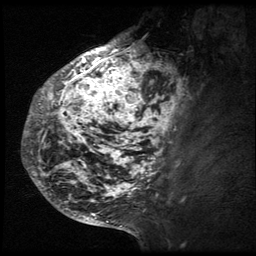
Breast MRI (dynamic contrast-enhanced), one sagittal slice. Slice 20 of 64 in the series (ordered by position). 3 images stored at this slice position (order not interpretable as contrast timing). 1.5 T. TE 4.2 ms, TR 9 ms. 2.5 mm slice thickness. 256 × 256 image matrix, field of view 180 × 180 mm. Patient: female, 50 years. From the clinical record (not read from this slice): setting: breast cancer imaged before/during neoadjuvant chemotherapy; receptor status: triple-negative.
Annotated regions visible in this slice (semi-automatically segmented with operator editing):
- analysis volume of interest (the breast-tissue region the enhancement analysis was run in; not a lesion): bounding box <24,39,194,212> (left, top, right, bottom; pixels)
- tumour enhancement mask (voxels above the 140 % enhancement threshold inside the analysis volume of interest): <24,39,187,209>